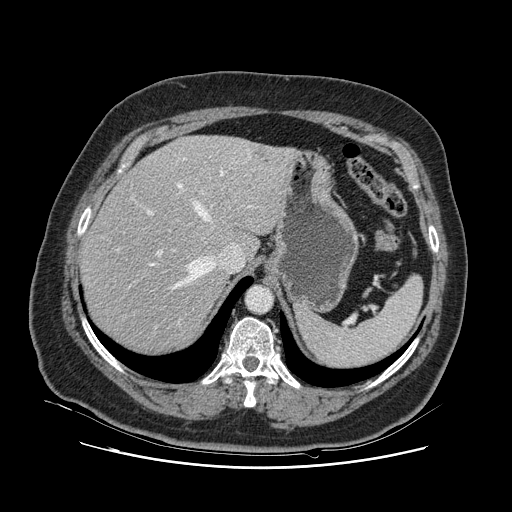
Contrast-enhanced abdominal CT, one axial slice; position 90 of 132 along the scan axis; 120 kVp; intravenous contrast given; soft-tissue window (W 400 / L 40 HU); 2.5 mm slice thickness; 512 × 512 image matrix, field of view 391 × 391 mm. Female patient, age 73 years. From the clinical record (not read from this slice): diagnosis: colorectal cancer liver metastases, imaged before liver resection; multiple liver metastases: no; largest metastasis: 7 cm; disease in both lobes: no.
Outlined on this slice (expert manual segmentation):
- hepatic veins: bounding box [x1, y1, x2, y2] px = [149, 154, 251, 289]
- liver: [83, 136, 290, 354]
- planned liver remnant (the part of the liver to remain after resection): [83, 160, 251, 354]
- portal vein (with intrahepatic branches): [116, 158, 185, 257]